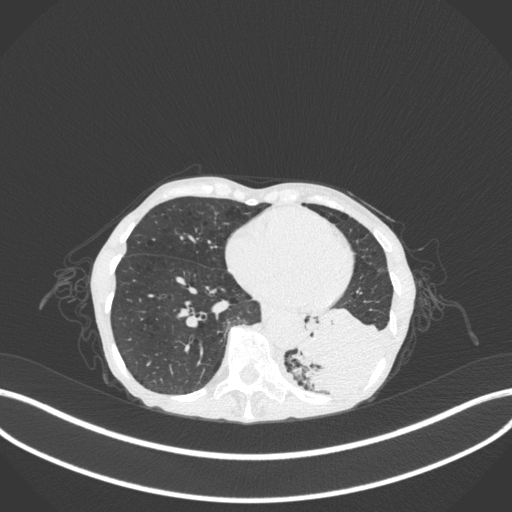
Chest CT, one axial slice; slice 83 of 347 in the series (ordered by position); 120 kVp; lung window (W 1500 / L -600 HU); 1 mm slice thickness; 512 × 512 image matrix. Patient: female, 70 years. From the clinical record (not read from this slice): clinical TNM (as recorded): T3 N0 M0.
Outlined on this slice (rectangle marked by the reading radiologist):
- lung tumour (recorded histology: small cell carcinoma): bounding box (x1, y1, x2, y2) in pixels: (293, 305, 392, 403)